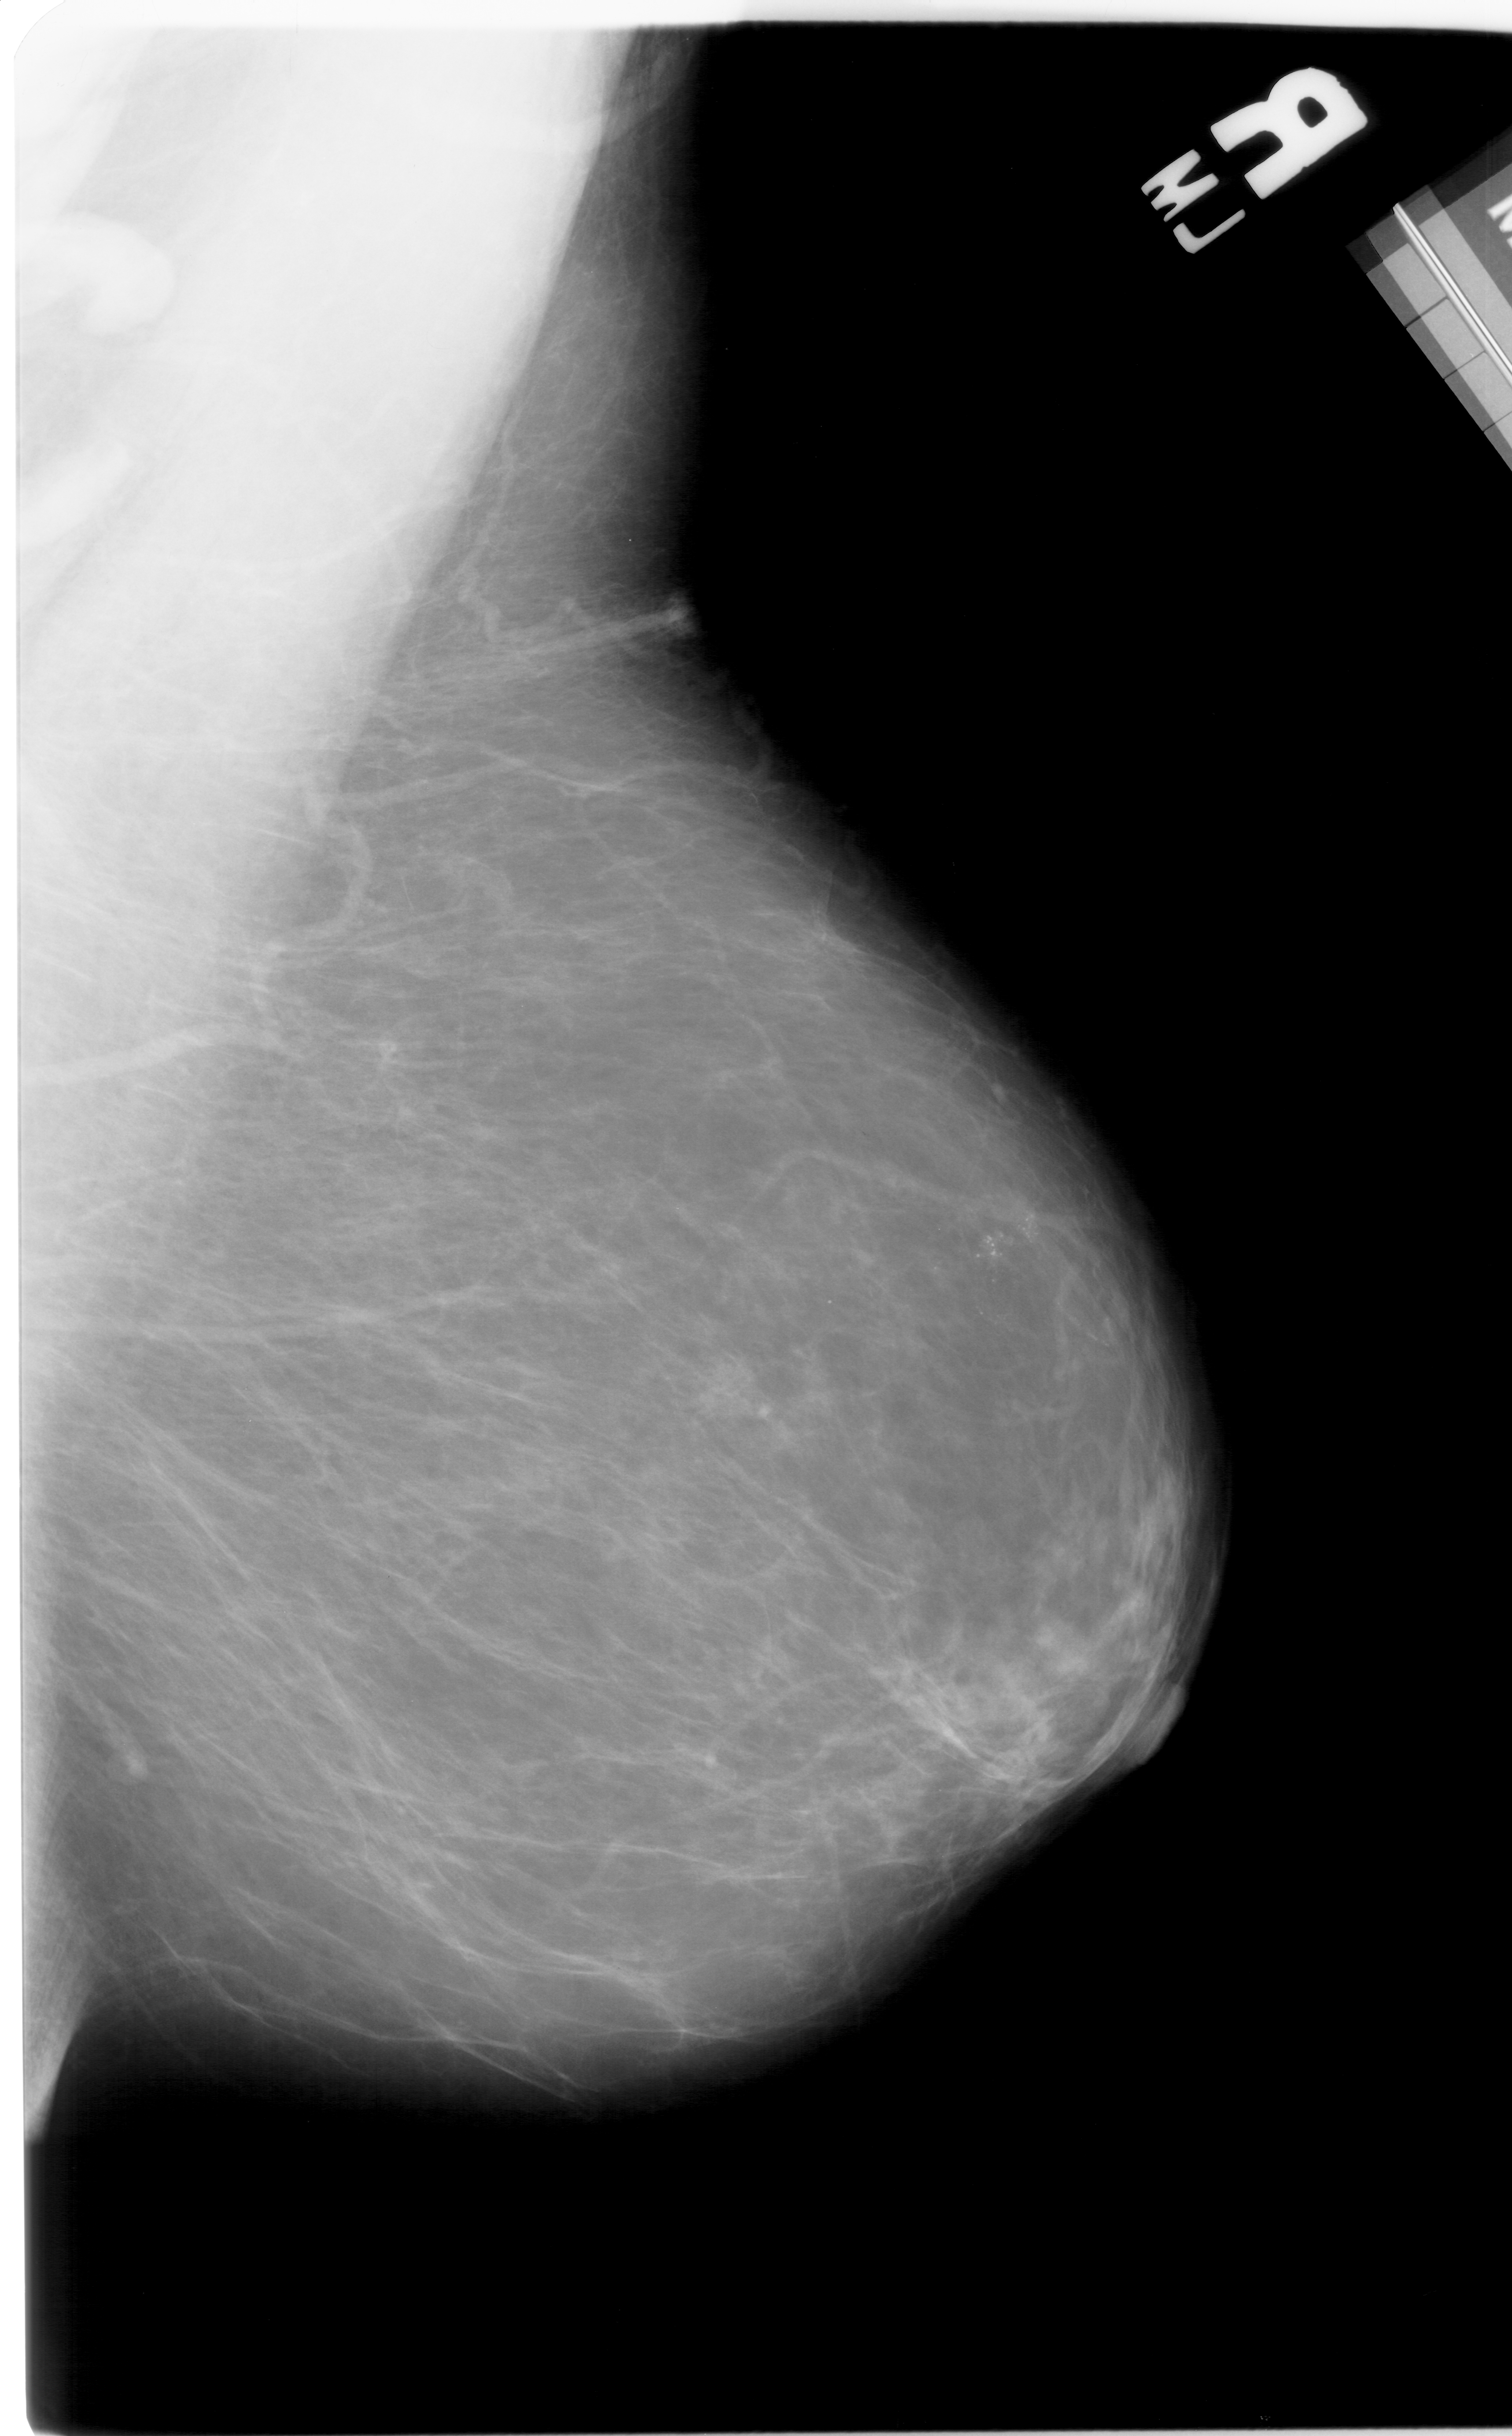
Digitized screen-film mammogram, right breast, mediolateral oblique (MLO) view, BI-RADS breast density category 2 (scale 1–4).
Abnormality record for this image: calcifications, morphology pleomorphic, distribution segmental; BI-RADS assessment category 4; pathology (as recorded): malignant.